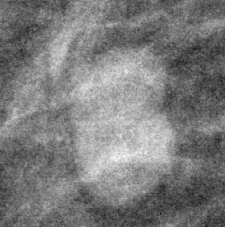
Crop from a digitized film mammogram around one marked abnormality, right breast, MLO view, BI-RADS breast density category 2 (scale 1–4).
Finding: mass, shape lobulated / lymph node, margins circumscribed; BI-RADS assessment category 2; benign without callback (not worked up further).